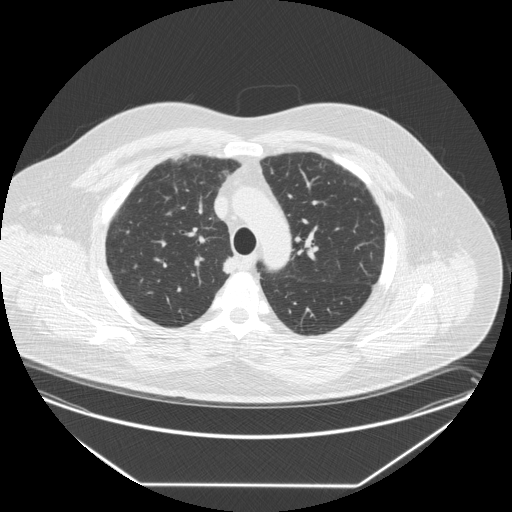
Low-dose screening chest CT, one axial slice. Slice 202 of 258 in the series (ordered by position). 120 kVp. Lung window (W 1500 / L -600 HU). 2.5 mm slice thickness. 512 × 512 image matrix, field of view 440 × 440 mm.
Outlined on this slice (expert manual segmentation):
- lesion 1 (tumor, upper lobe of right lung): bounding box [x1, y1, x2, y2] px = [223, 256, 237, 274]